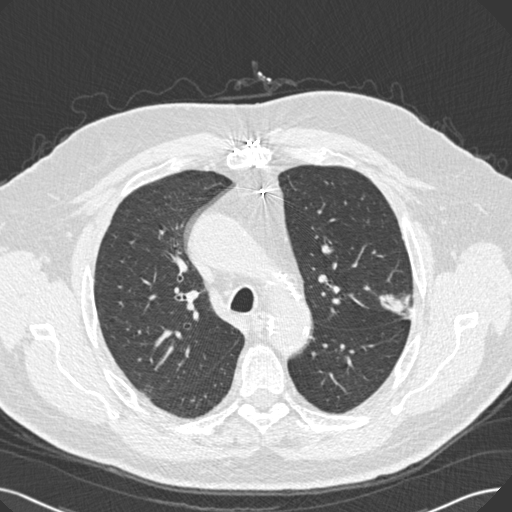
Low-dose screening chest CT, one axial slice; position 183 of 269 along the scan axis; 120 kVp; lung window (W 1500 / L -600 HU); 1 mm slice thickness; 512 × 512 image matrix, field of view 370 × 370 mm.
Structures marked on this image (manually delineated by an expert):
- lesion 1 (tumor, upper lobe of left lung): bounding box <379,294,411,320> (left, top, right, bottom; pixels)